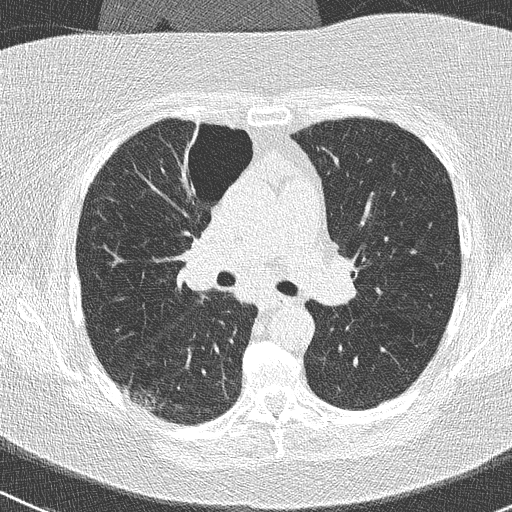
Low-dose screening chest CT, one axial slice. Slice 161 of 261 in the series (ordered by position). Lung window (W 1500 / L -600 HU). 2 mm slice thickness. 512 × 512 image matrix.
Structures marked on this image (expert manual segmentation):
- lesion 1 (tumor, lower lobe of right lung): bounding box <135,394,155,409> (left, top, right, bottom; pixels)